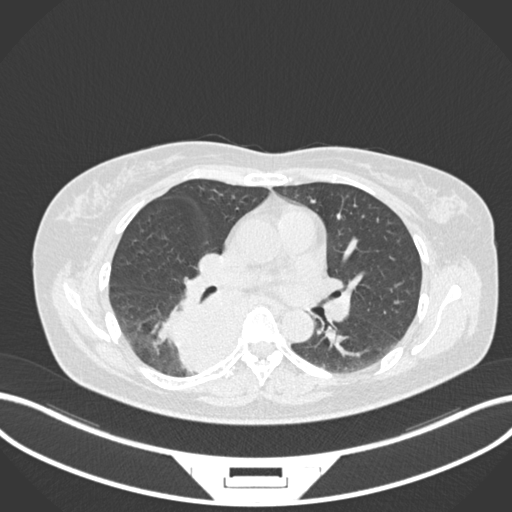
Chest CT, one axial slice; position 597 of 677 along the scan axis; lung window (W 1500 / L -600 HU); 1 mm slice thickness; 512 × 512 image matrix, field of view 400 × 400 mm. Patient: female, 54 years. Case-level facts recorded for this patient, not image findings: clinical TNM (as recorded): T4 N0 M0.
Annotated regions visible in this slice (rectangle marked by the reading radiologist):
- lung tumour (recorded histology: adenocarcinoma): bounding box [x1, y1, x2, y2] px = [164, 280, 250, 376]